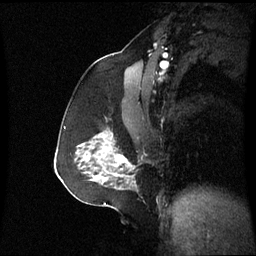
Breast MRI (dynamic contrast-enhanced), one sagittal slice; position 35 of 60 along the scan axis; dynamic contrast-enhanced series, image 2 of 3 at this slice position (ordered by acquisition); 1.5 T; TE 4.2 ms, TR 8.9 ms; 2.4 mm slice thickness; 256 × 256 image matrix, field of view 230 × 230 mm. Female patient, age 59 years. Case-level facts recorded for this patient, not image findings: setting: breast cancer imaged before/during neoadjuvant chemotherapy; receptor status: triple-negative.
Structures marked on this image (semi-automatic segmentation, software-assisted and operator-edited):
- analysis volume of interest (the breast-tissue region the enhancement analysis was run in; not a lesion): bounding box <86,131,136,183> (left, top, right, bottom; pixels)
- tumour enhancement mask (voxels above the 70 % enhancement threshold inside the analysis volume of interest): <115,155,129,165>